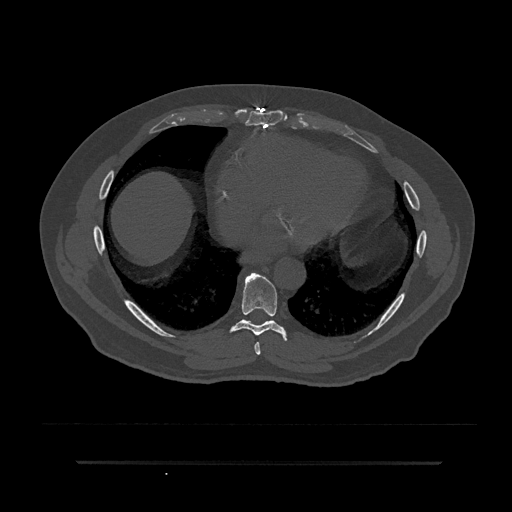
CT including the spine, one axial slice; slice 428 of 797 in the series (ordered by position); reconstruction kernel Br40s/3; 120 kVp; bone window (W 1800 / L 400 HU); 0.5 mm slice thickness; 512 × 512 image matrix, field of view 464 × 464 mm. Male patient, age 59 years. Case-level facts recorded for this patient, not image findings: primary cancer: bile ducts.
Structures marked on this image (semi-automatic segmentation, software-assisted and operator-edited):
- T7 vertebra: bounding box <254,342,261,355> (left, top, right, bottom; pixels)
- T8 vertebra: <230,273,287,341>